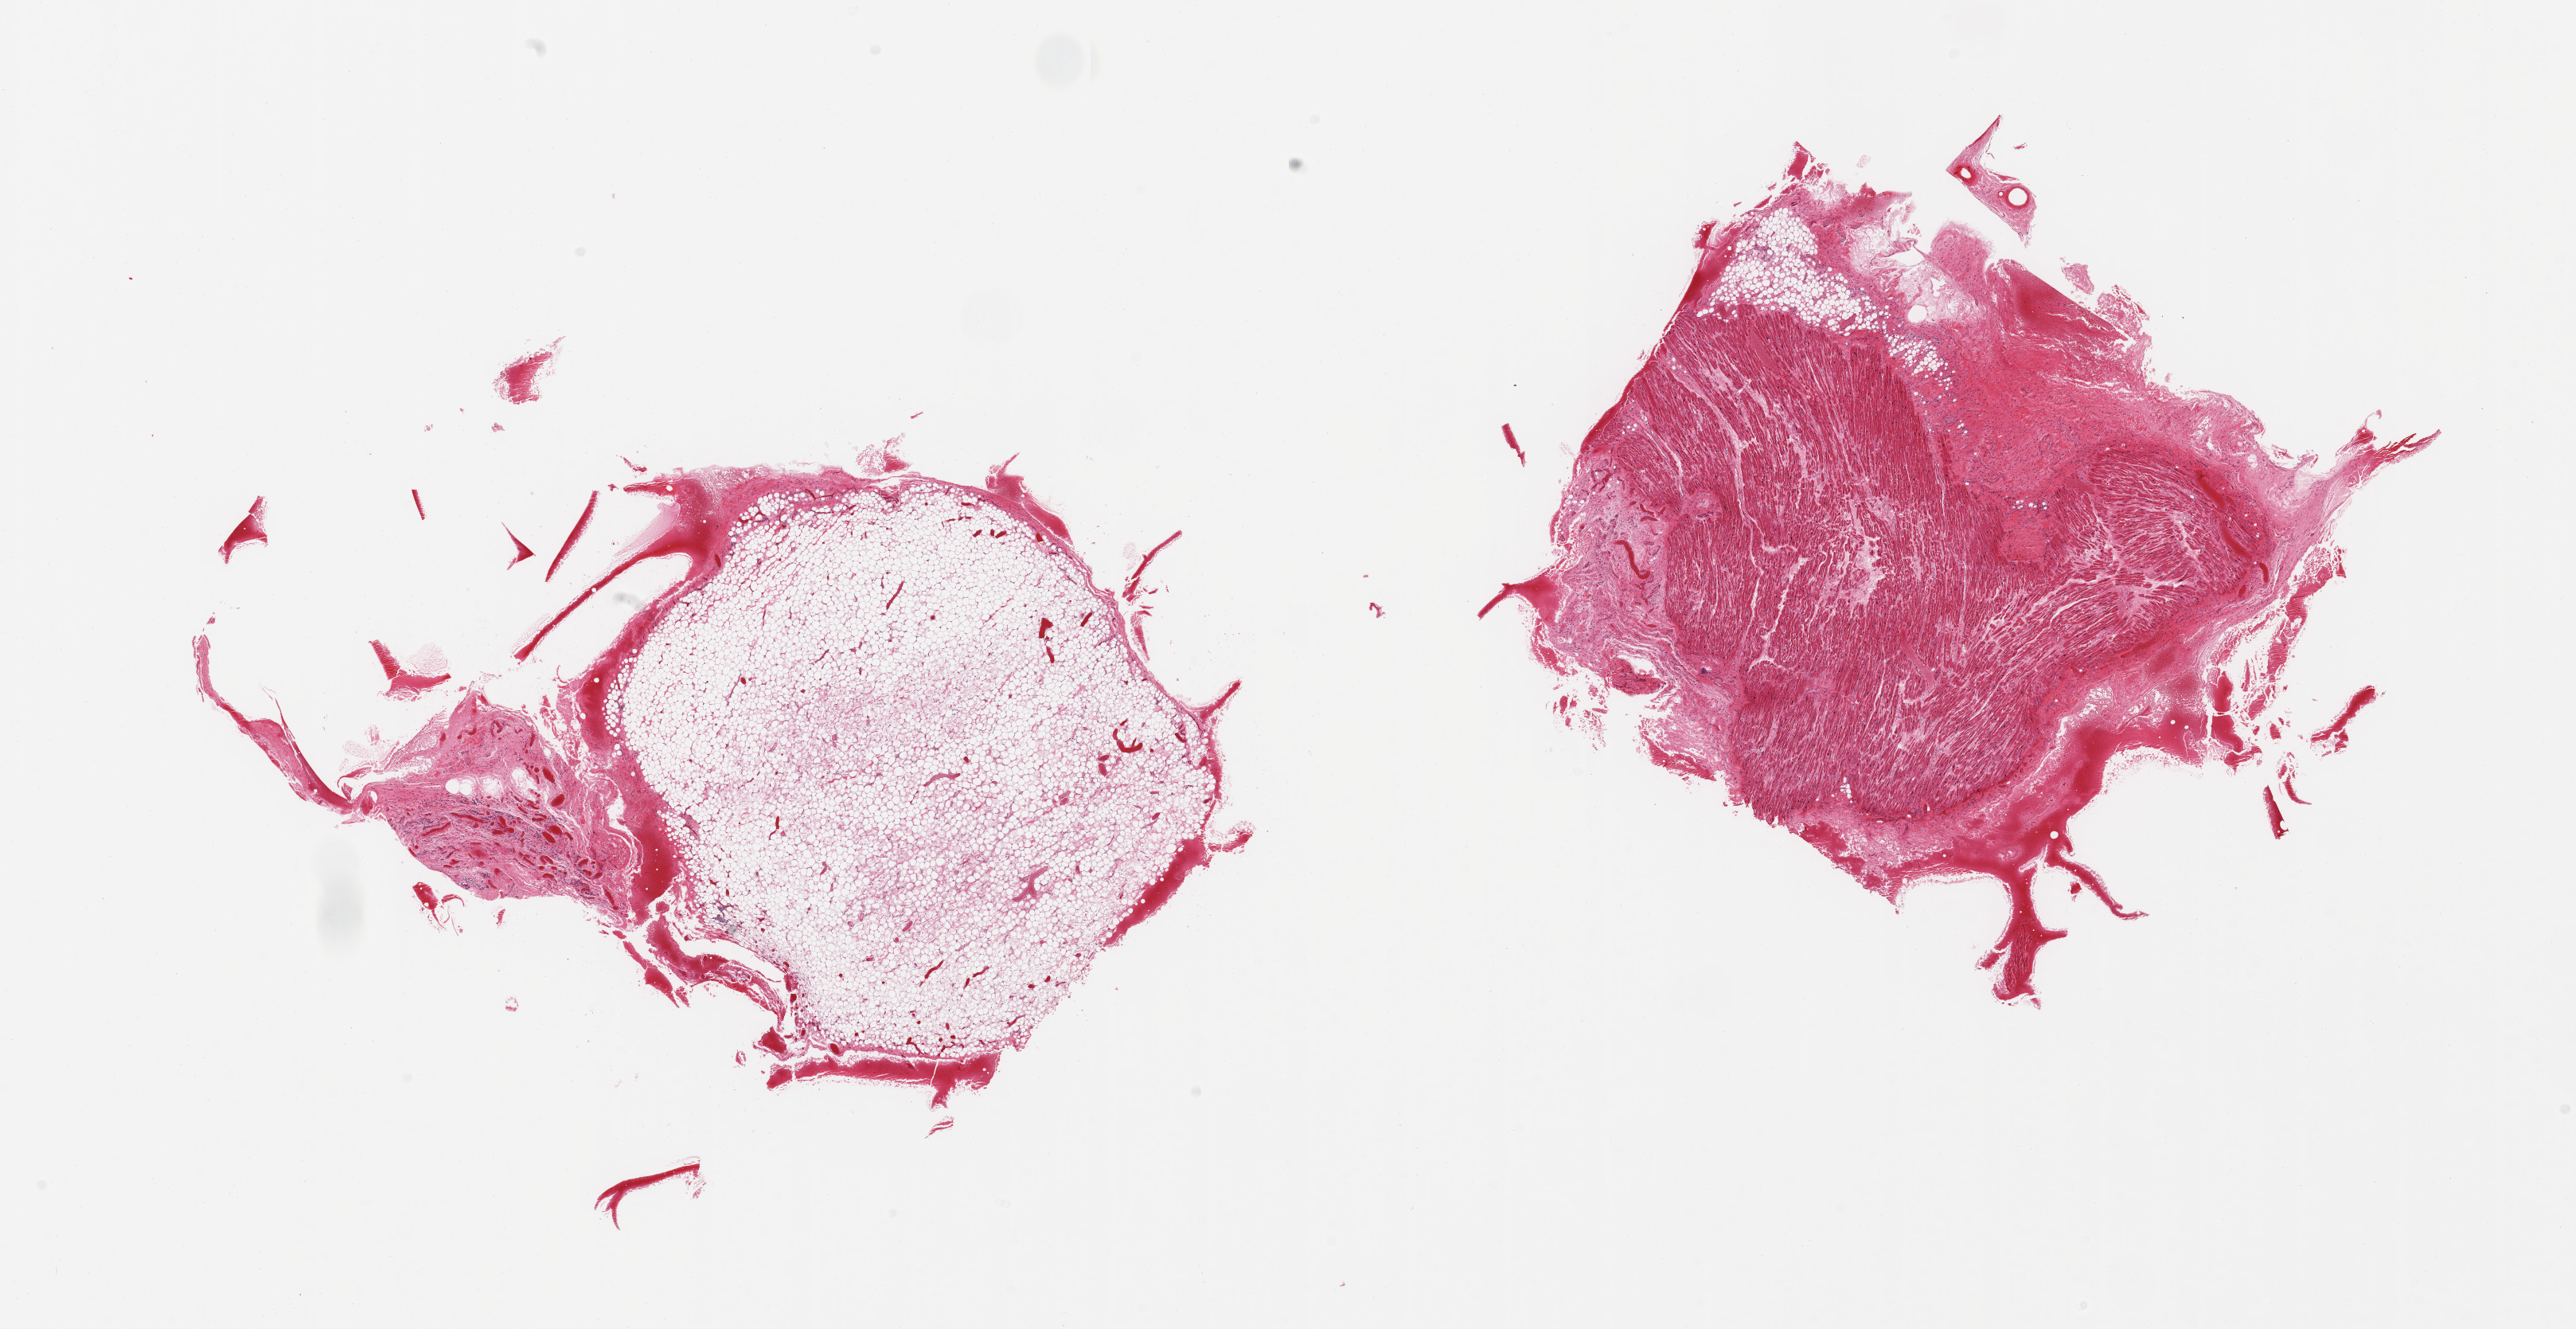
Digitized H&E-stained section, brightfield, whole scanned area (about 25.6 x 13.2 mm, slide scanned at 20x) shown as a low-resolution overview, PAXgene-fixed paraffin-embedded (PFPE) section, target tissue: auricular appendage, tissue donor sample. Donor: male.
- review note (as recorded): 2 pieces; 1 piece is all fat